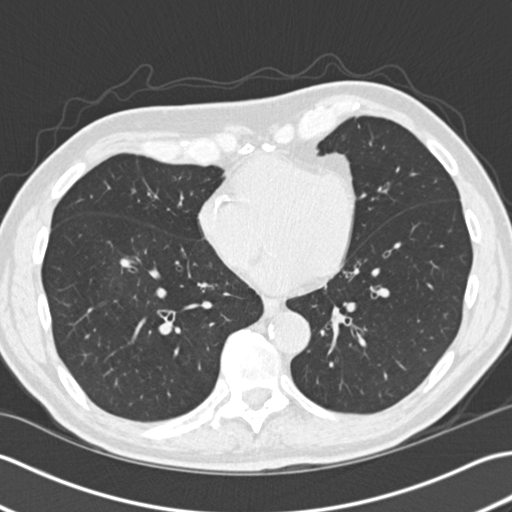
Low-dose screening chest CT, one axial slice; 120 kVp; lung window (W 1500 / L -600 HU); 2 mm slice thickness; 512 × 512 image matrix.
Outlined on this slice (expert manual segmentation):
- lesion 1 (tumor, lower lobe of right lung): bounding box <120,258,133,268> (left, top, right, bottom; pixels)